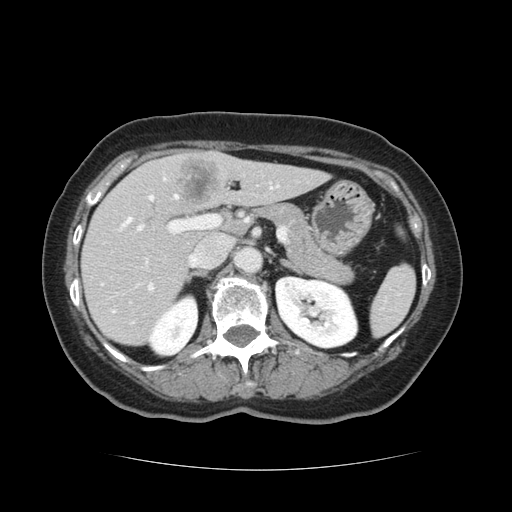
Contrast-enhanced abdominal CT, one axial slice. Slice 69 of 128 in the series (ordered by position). Intravenous contrast given. Soft-tissue window (W 400 / L 40 HU). 2.5 mm slice thickness. 512 × 512 image matrix, field of view 366 × 366 mm. Female patient, age 67 years. From the clinical record (not read from this slice): diagnosis: colorectal cancer liver metastases, imaged before liver resection; multiple liver metastases: yes; largest metastasis: 3 cm; disease in both lobes: yes.
Structures marked on this image (manually delineated by an expert):
- hepatic veins: bounding box <113,186,279,312> (left, top, right, bottom; pixels)
- liver: <83,151,325,345>
- planned liver remnant (the part of the liver to remain after resection): <83,162,325,345>
- portal vein (with intrahepatic branches): <137,182,272,292>
- liver metastasis: <175,156,220,207>